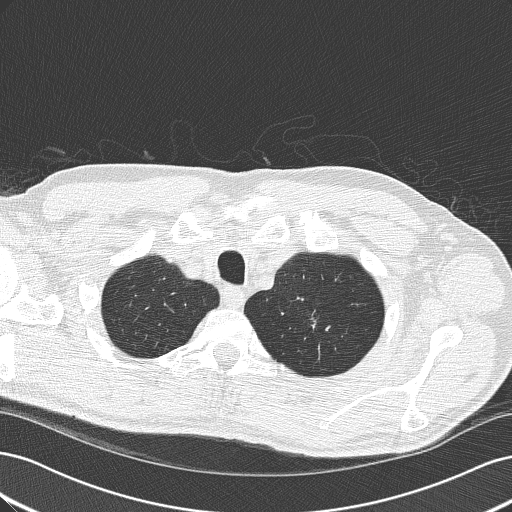
Chest CT (low-dose screening protocol), one axial image, third screening round (two years after baseline), lung window (W 1500 / L -600 HU), lung (sharp) reconstruction kernel (B50f), slice 31 of 192 in the series. Male, age 64 years at enrolment. Former smoker at enrolment.
- Lesion marked by an expert reader, bounding box [x1, y1, x2, y2] px = [290, 304, 331, 343].
- Reader record for this screening exam (exam-level; its link to the box is not recorded): non-calcified nodule or mass ≥4 mm, left upper lobe, 8 × 8 mm, smooth margins, soft tissue attenuation, pre-existing on the prior screen: yes; interval growth: yes.
- Participant outcome: lung cancer diagnosed 111 days after this screen — adenocarcinoma, NOS, left upper lobe, poorly differentiated (G3), stage IA (AJCC 6th edition), 10 mm at pathology.